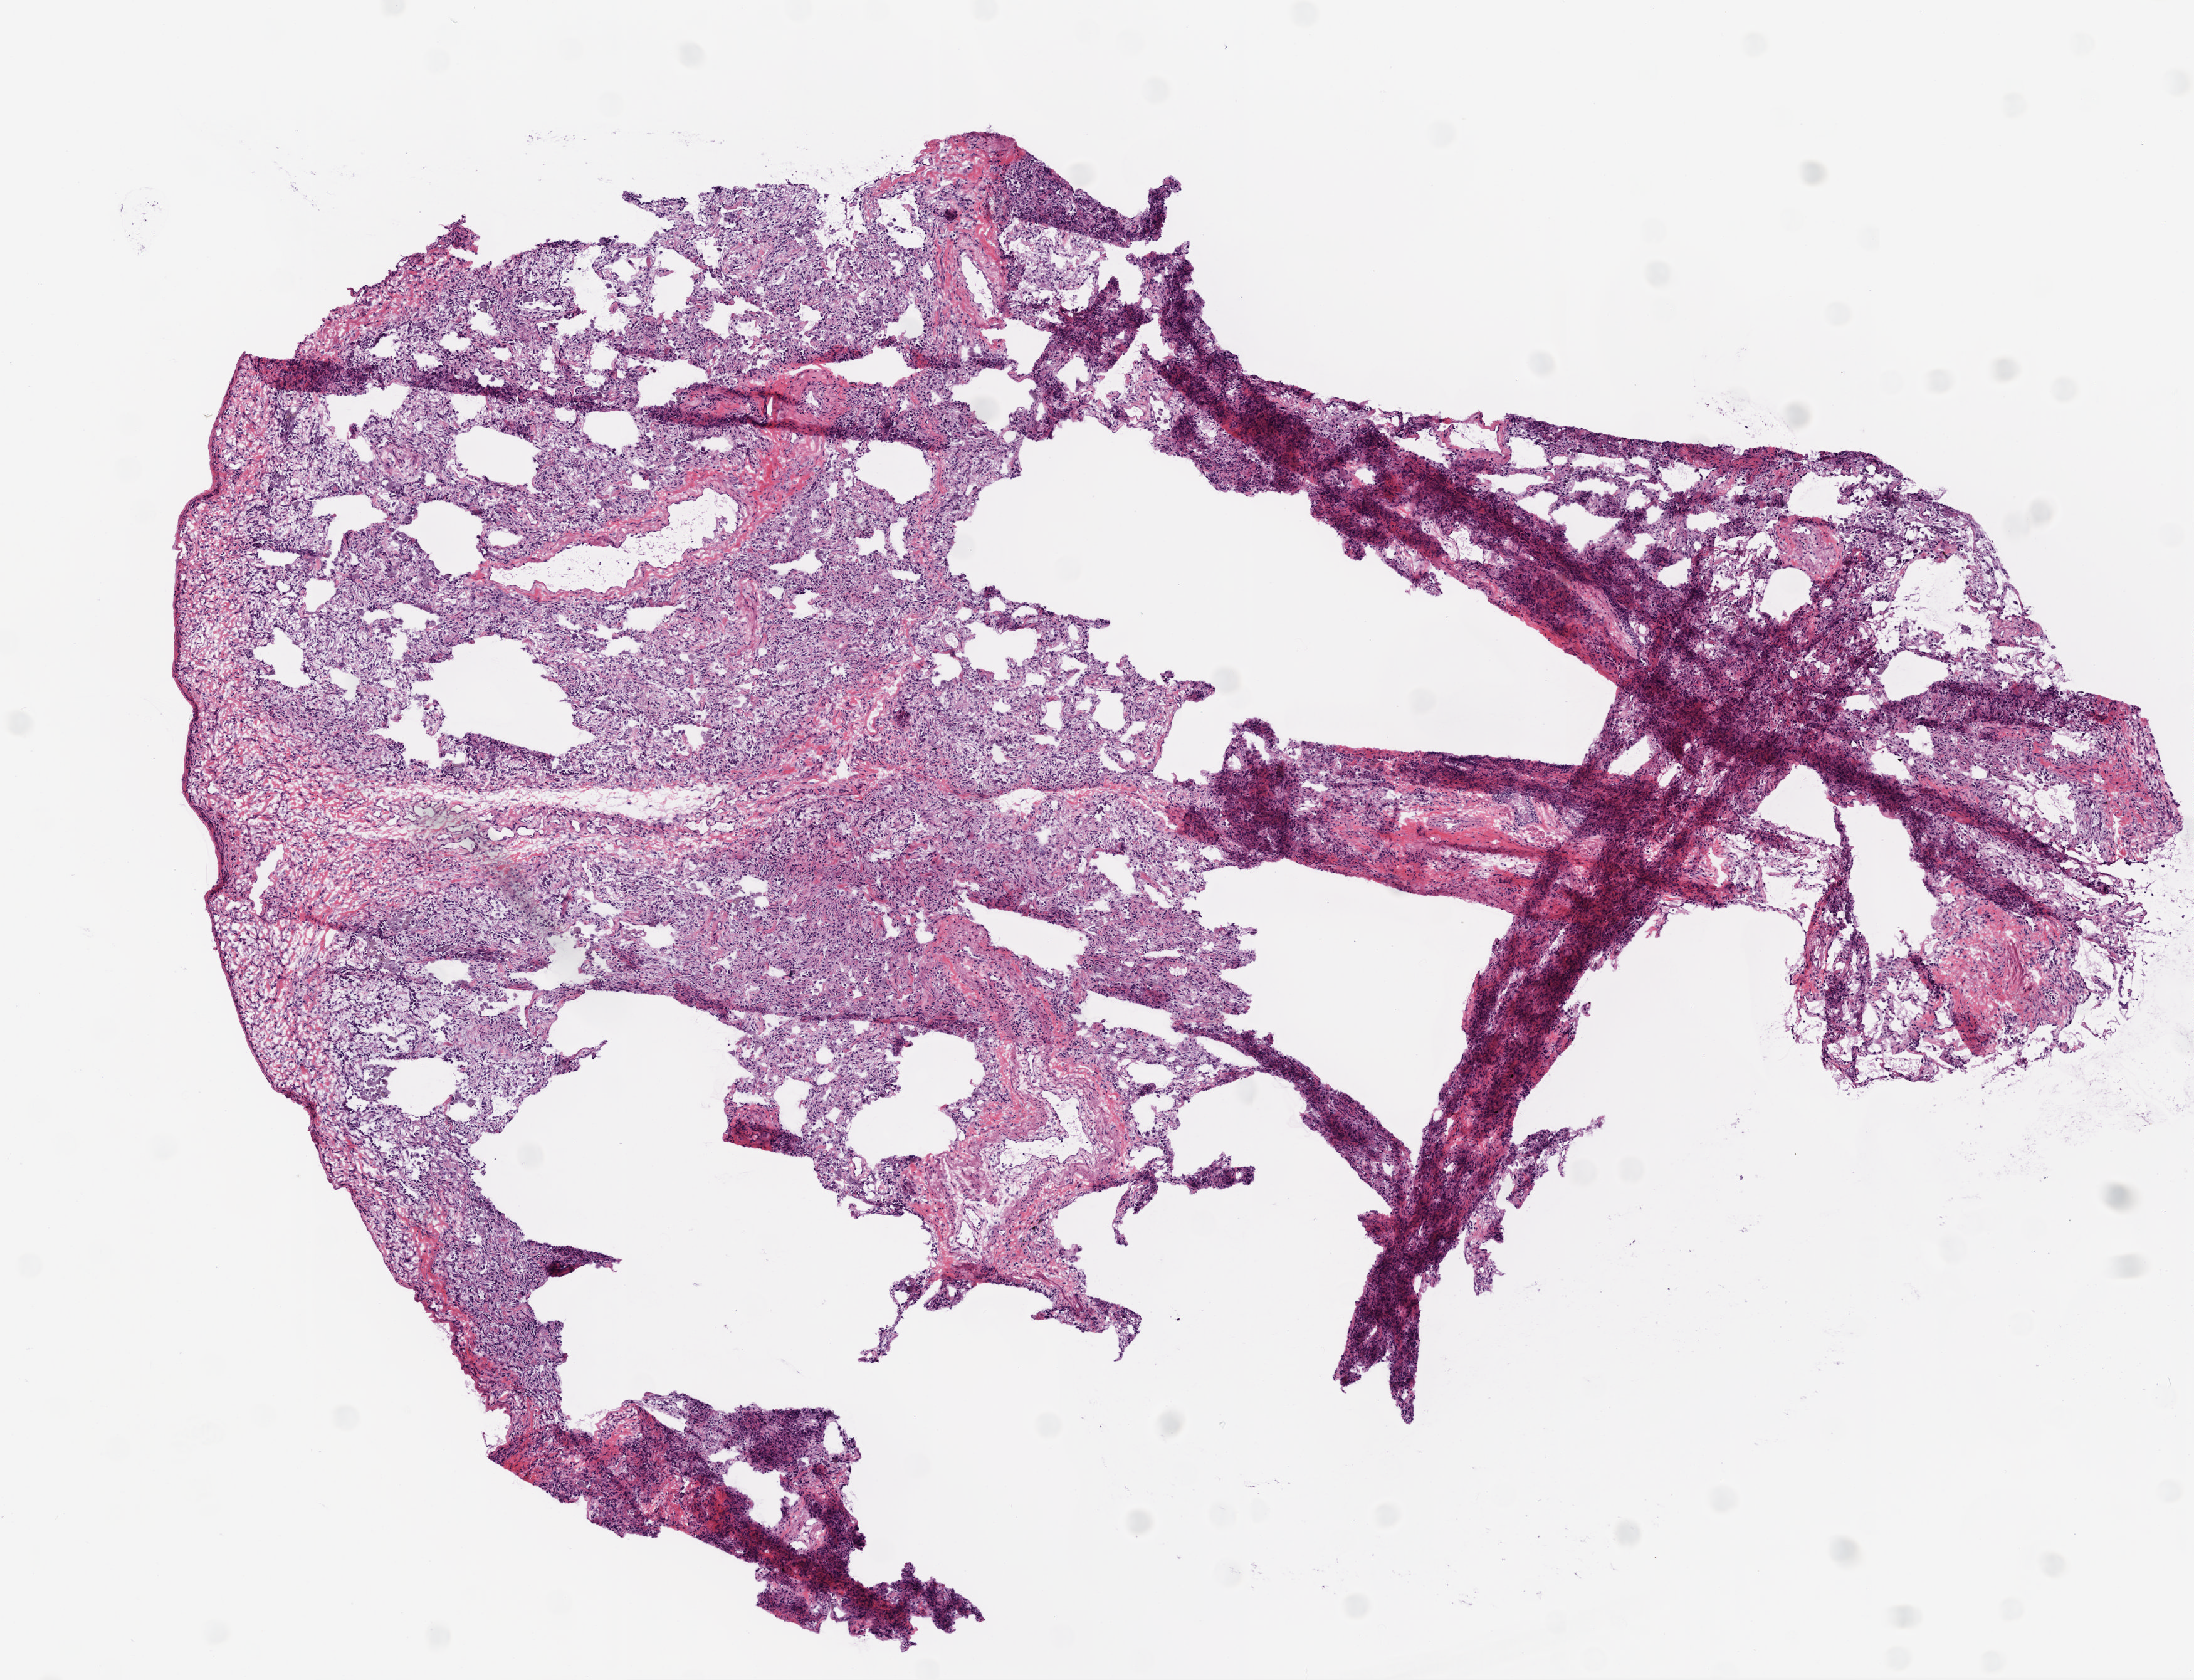
H&E-stained whole-slide image, low-resolution overview of the scanned area, about 7.0 x 5.4 mm, frozen section from the top of the tissue portion, solid tissue normal (non-tumour tissue) sample from the lung. Male patient; age at initial diagnosis 58 years.
* this section: solid tissue normal sample (biorepository sample class)
* patient diagnosis: Squamous cell carcinoma, NOS (lower lobe, lung)